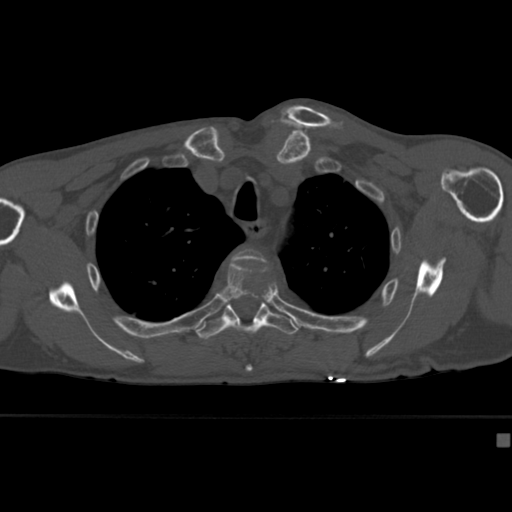
CT including the spine, one axial slice; position 317 of 430 along the scan axis; 120 kVp; bone window (W 1800 / L 400 HU); 512 × 512 image matrix, field of view 337 × 337 mm. Male patient, age 64 years. From the clinical record (not read from this slice): primary cancer: uterus; vertebrae with lytic lesions (as recorded): T1, T4, T5, T7, L5.
Structures marked on this image (semi-automatic segmentation, software-assisted and operator-edited):
- T3 vertebra: bounding box [x1, y1, x2, y2] px = [232, 249, 267, 263]
- T4 vertebra: [219, 259, 279, 372]
- T5 vertebra: [196, 299, 299, 340]